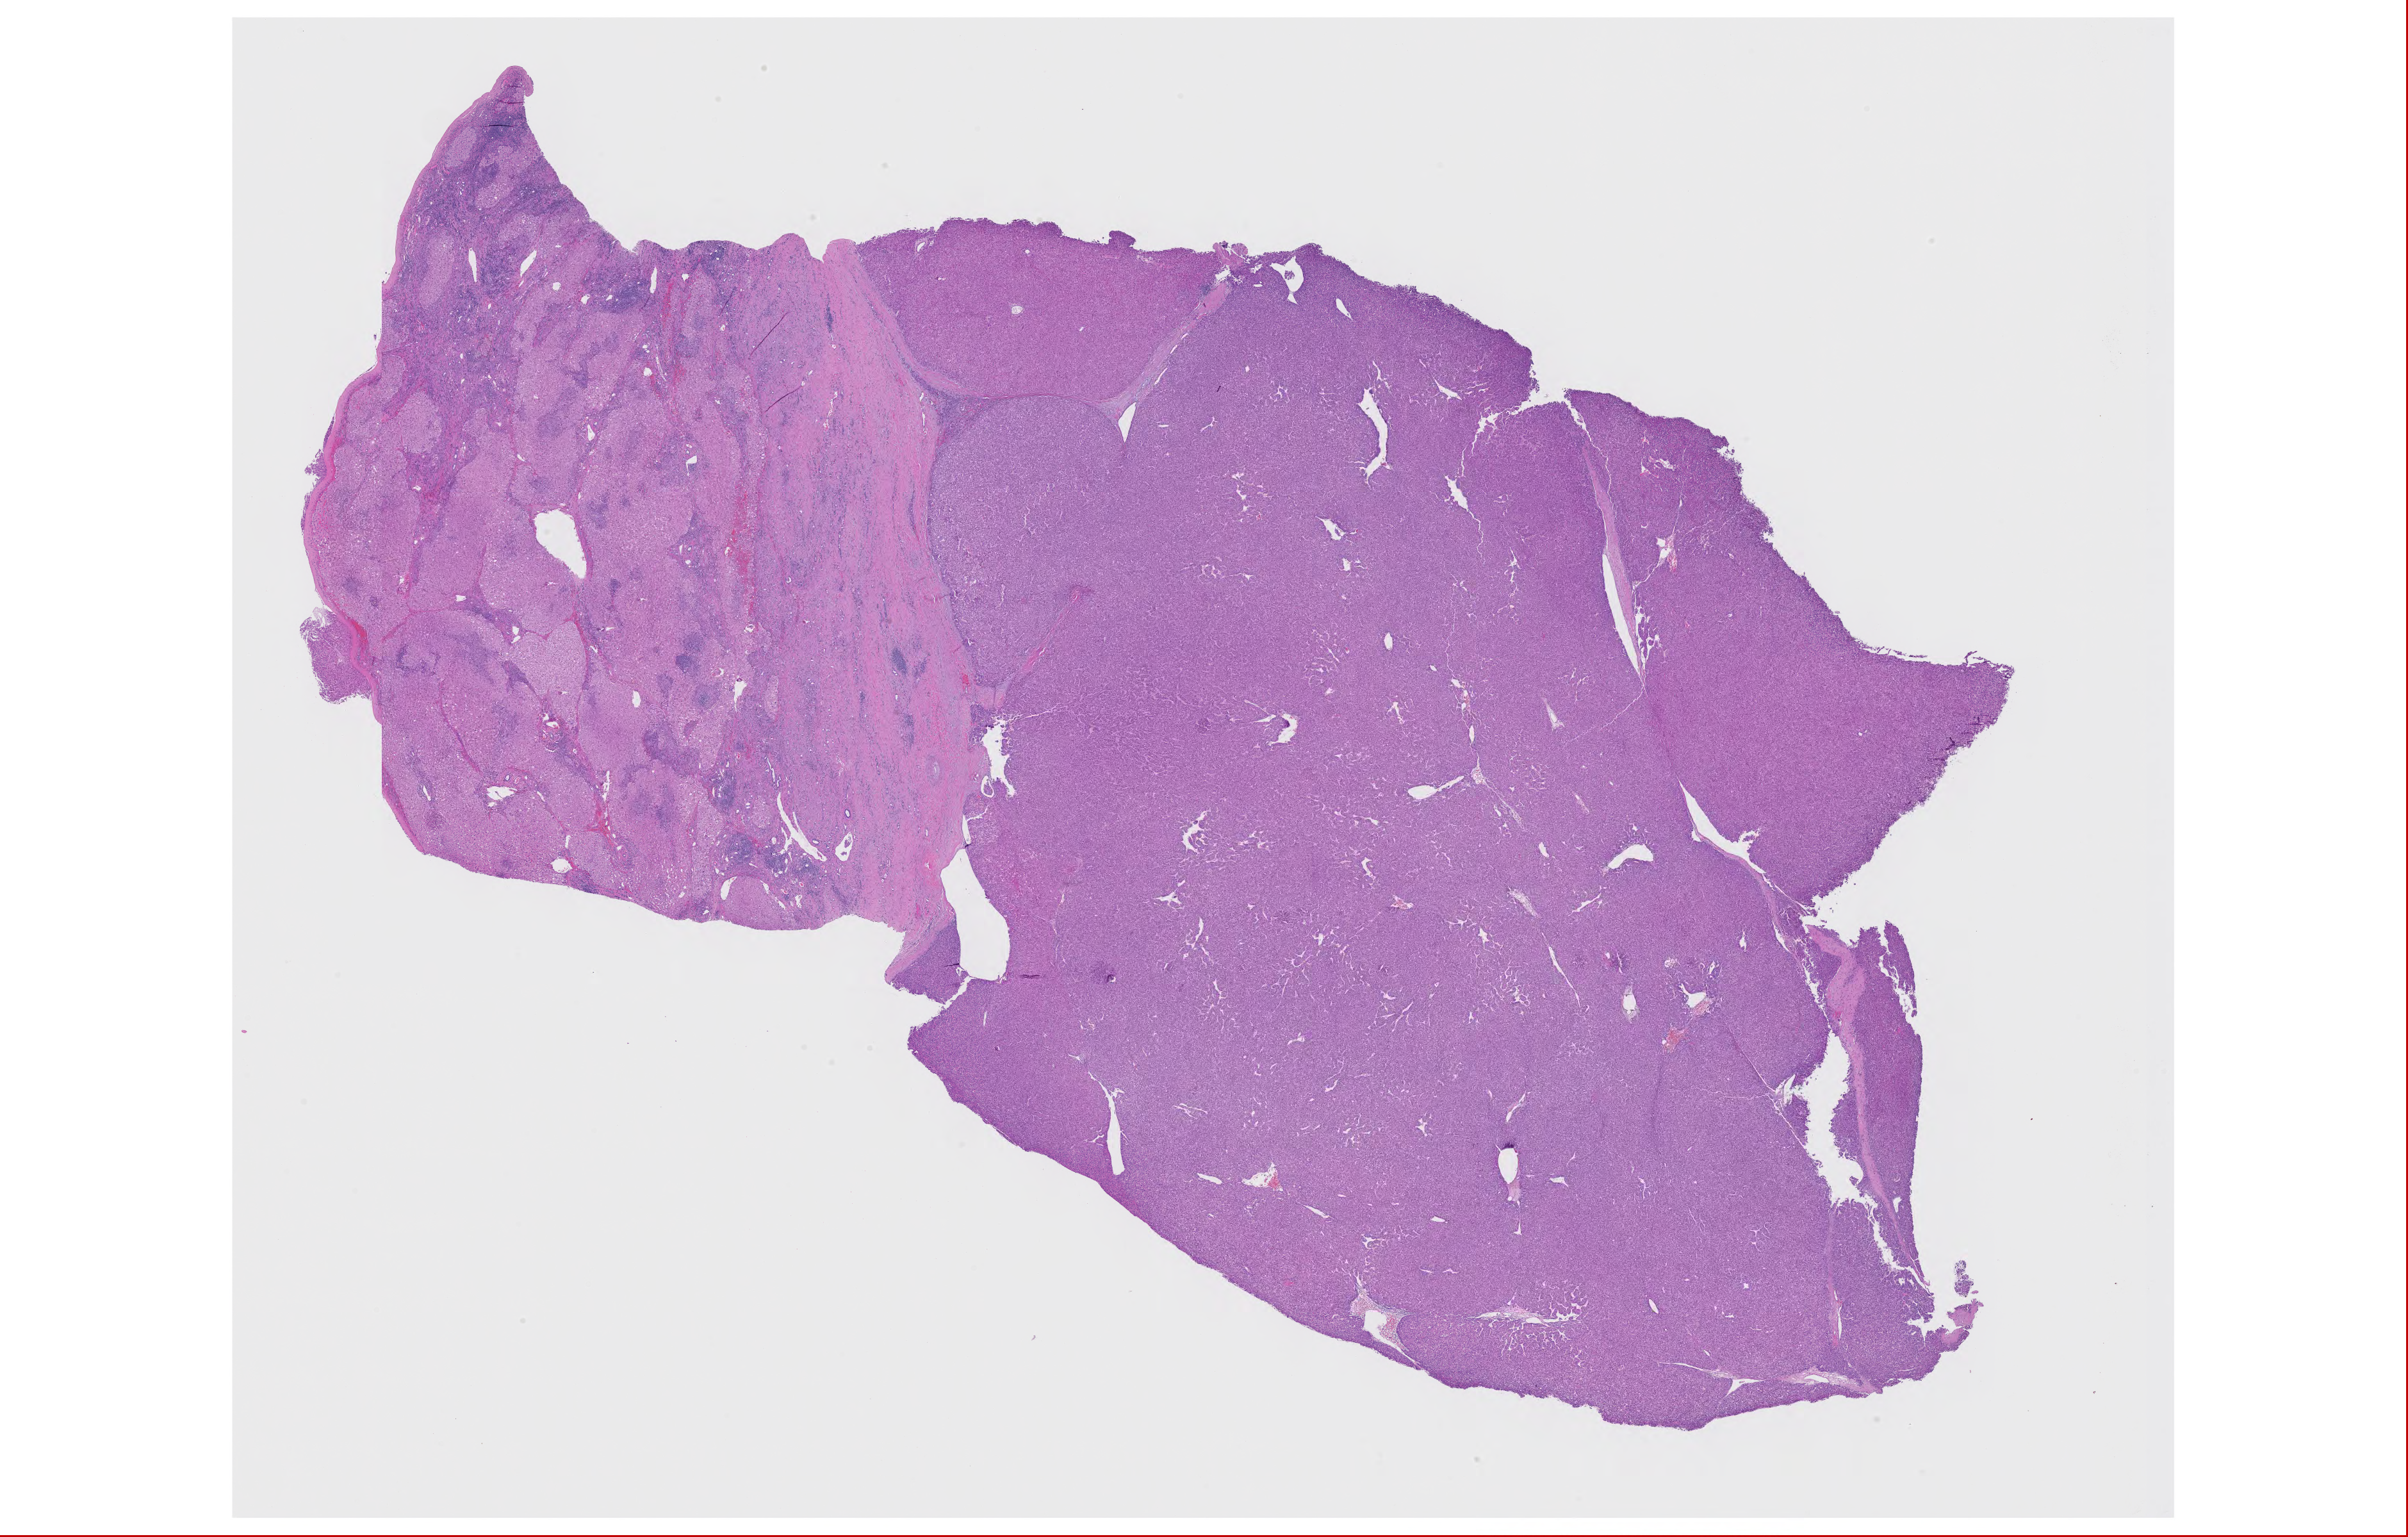
Whole-slide histology image, H&E, a low-resolution overview of the entire scanned area, about 30.1 x 19.2 mm (slide scanned at 20x), formalin-fixed paraffin-embedded (FFPE) diagnostic section, primary tumour sample from the liver. Patient: female, age at initial diagnosis 68 years. Histologic grade: G1 (well differentiated).
- histologic diagnosis: Hepatocellular carcinoma, NOS
- AJCC pathologic stage: II (7th edition)